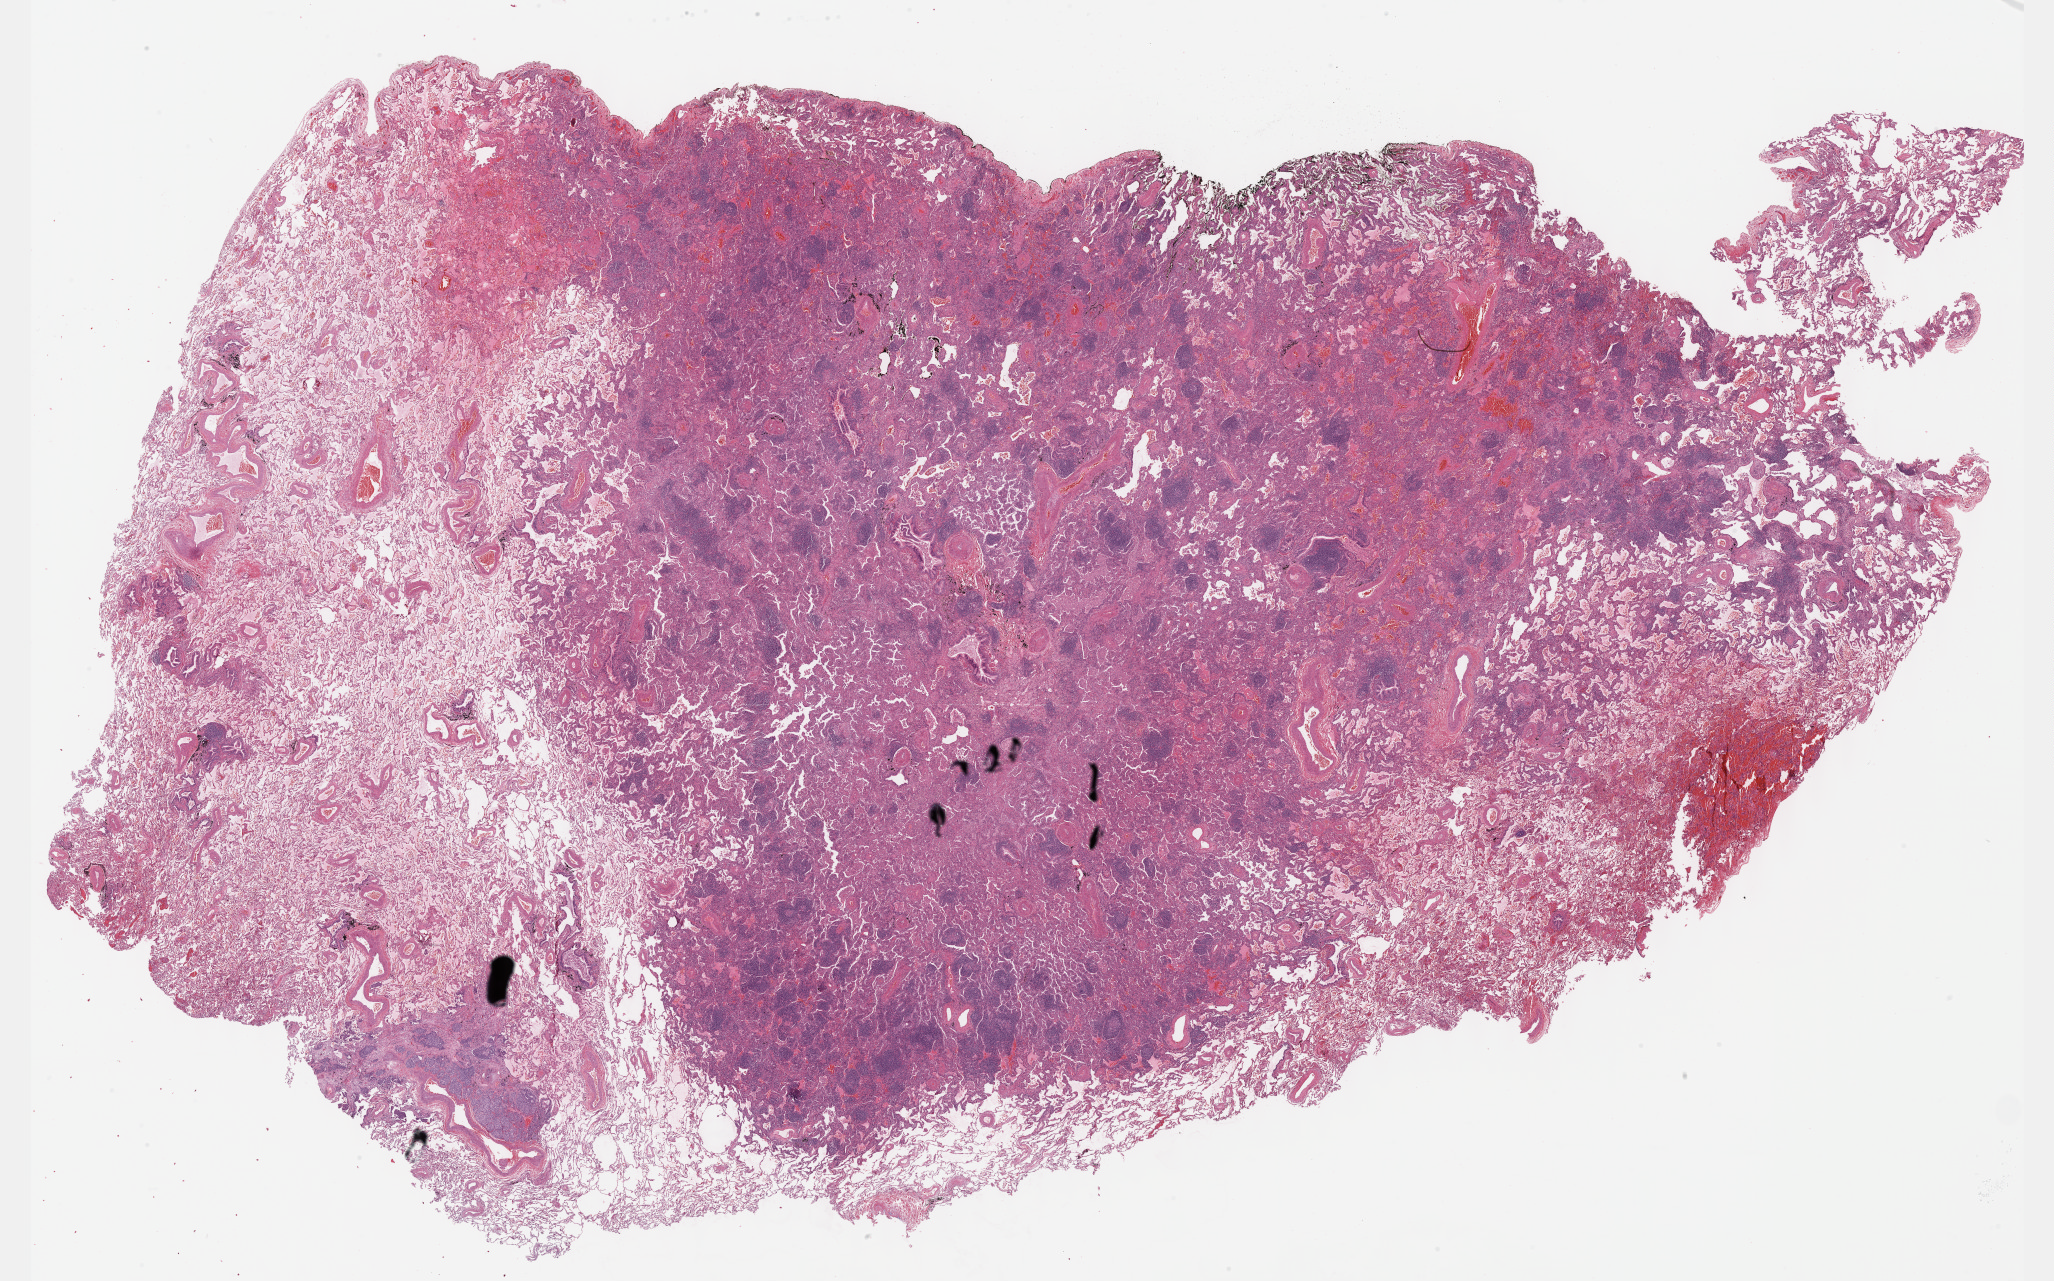
Whole-slide histology image, Hematoxylin and eosin (H&E) stained, shown as a low-resolution overview of the whole scanned area (about 33.2 x 20.7 mm, slide scanned at 40x), formalin-fixed paraffin-embedded (FFPE) diagnostic section, sample: primary tumour, lung. Female, age 79 years at initial diagnosis.
Pathologic diagnosis: Adenocarcinoma with mixed subtypes (lower lobe, lung).